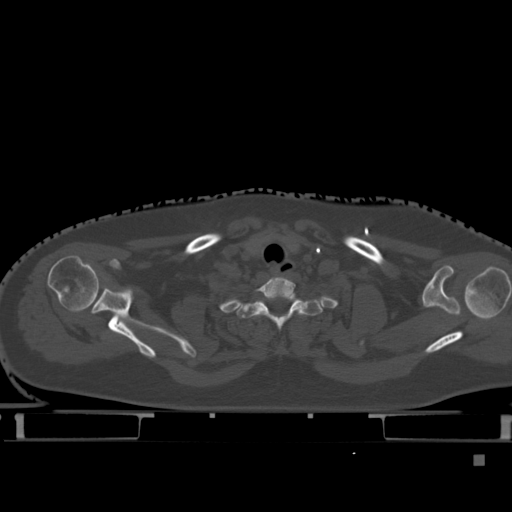
CT including the spine, one axial slice; slice 374 of 495 in the series (ordered by position); bone window (W 1800 / L 400 HU); 1.5 mm slice thickness; 512 × 512 image matrix, field of view 404 × 404 mm. Patient: female, 33 years. Case-level facts recorded for this patient, not image findings: primary cancer: breast; vertebrae with lytic lesions (as recorded): T1.
Outlined on this slice (semi-automatic segmentation, software-assisted and operator-edited):
- T1 vertebra: bounding box <237,292,322,331> (left, top, right, bottom; pixels)